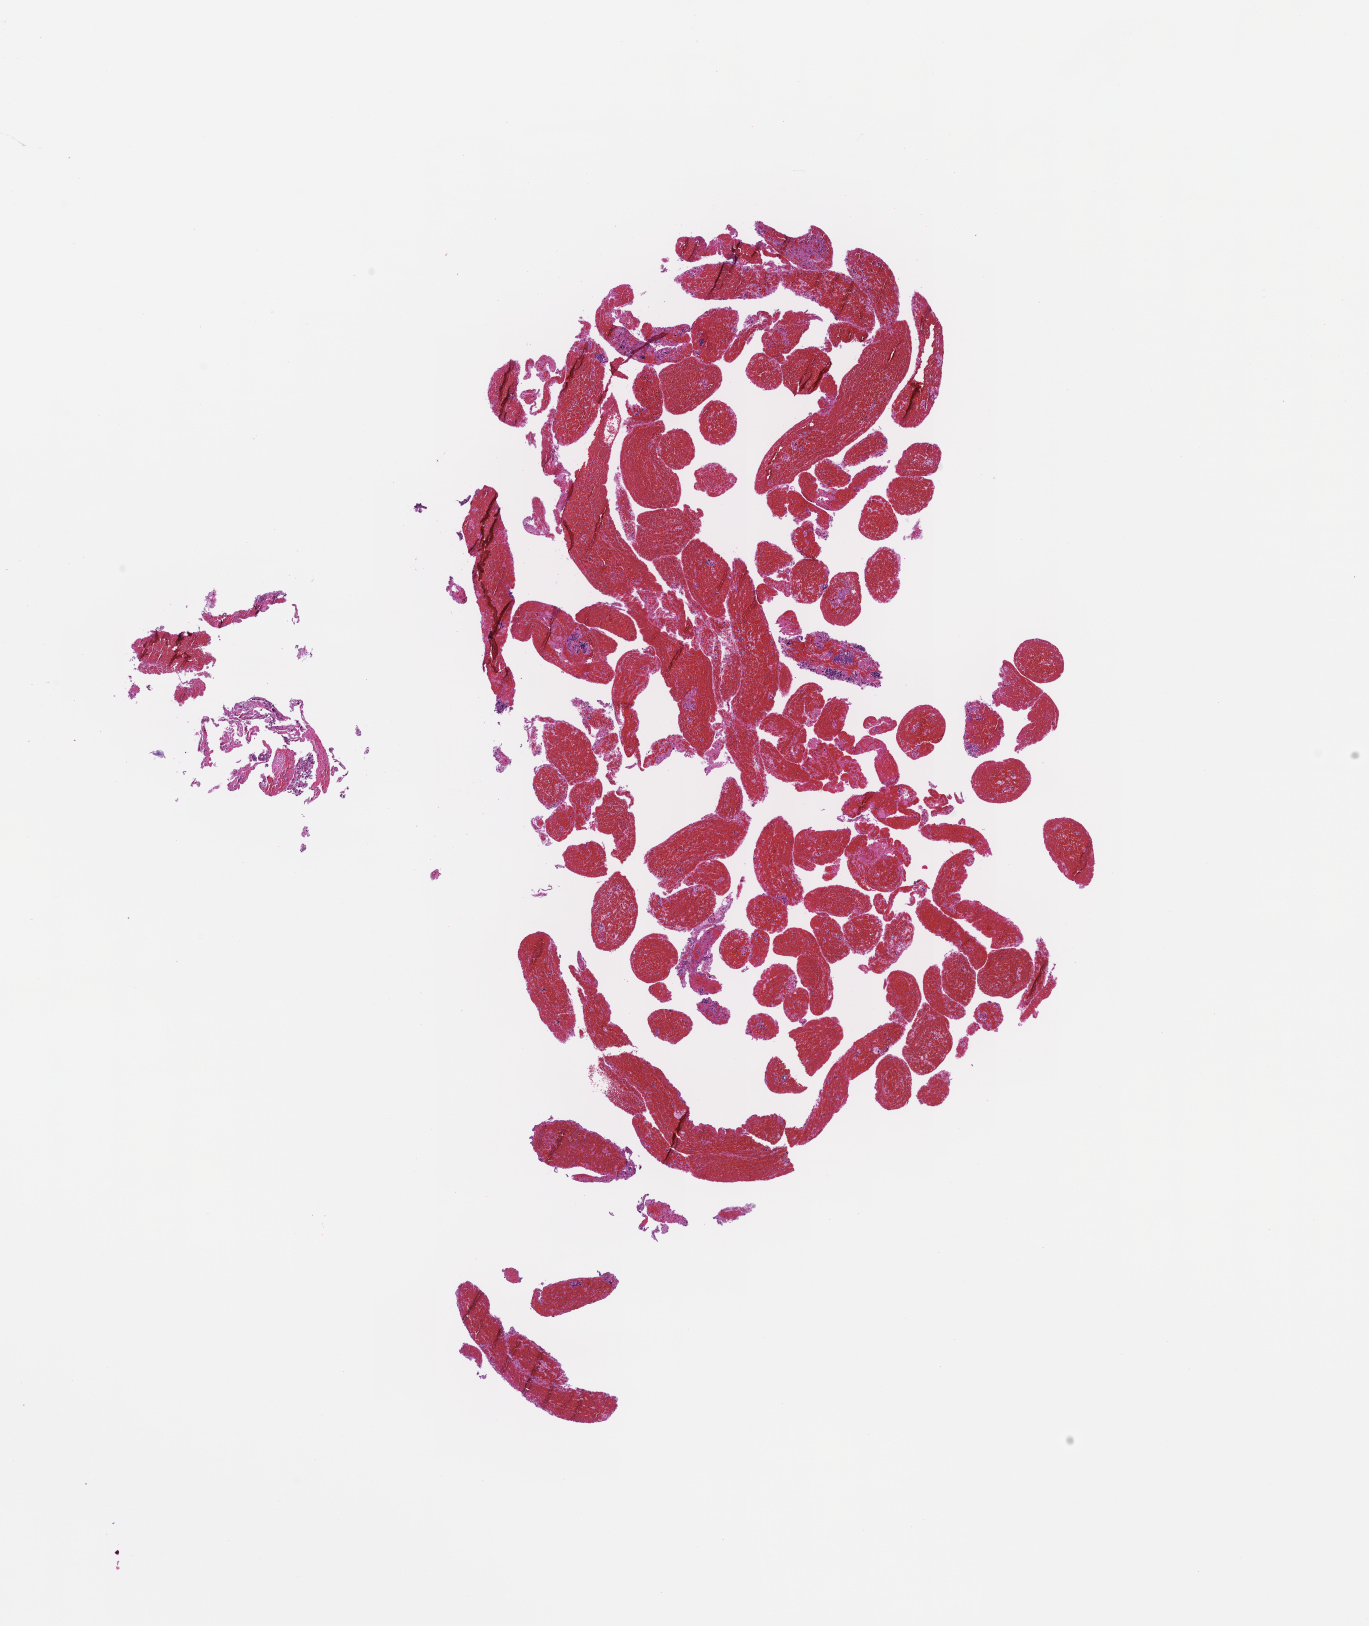
Digitized hematoxylin and eosin (H&E)-stained section — shown as a low-resolution overview of the whole scanned area (about 11.1 x 13.1 mm). Formalin-fixed, paraffin-embedded (FFPE) tissue. Archival tissue. Patient: female.
• this section: metastatic tumor tissue
• patient diagnosis (primary): Non-Small Cell Lung Carcinoma